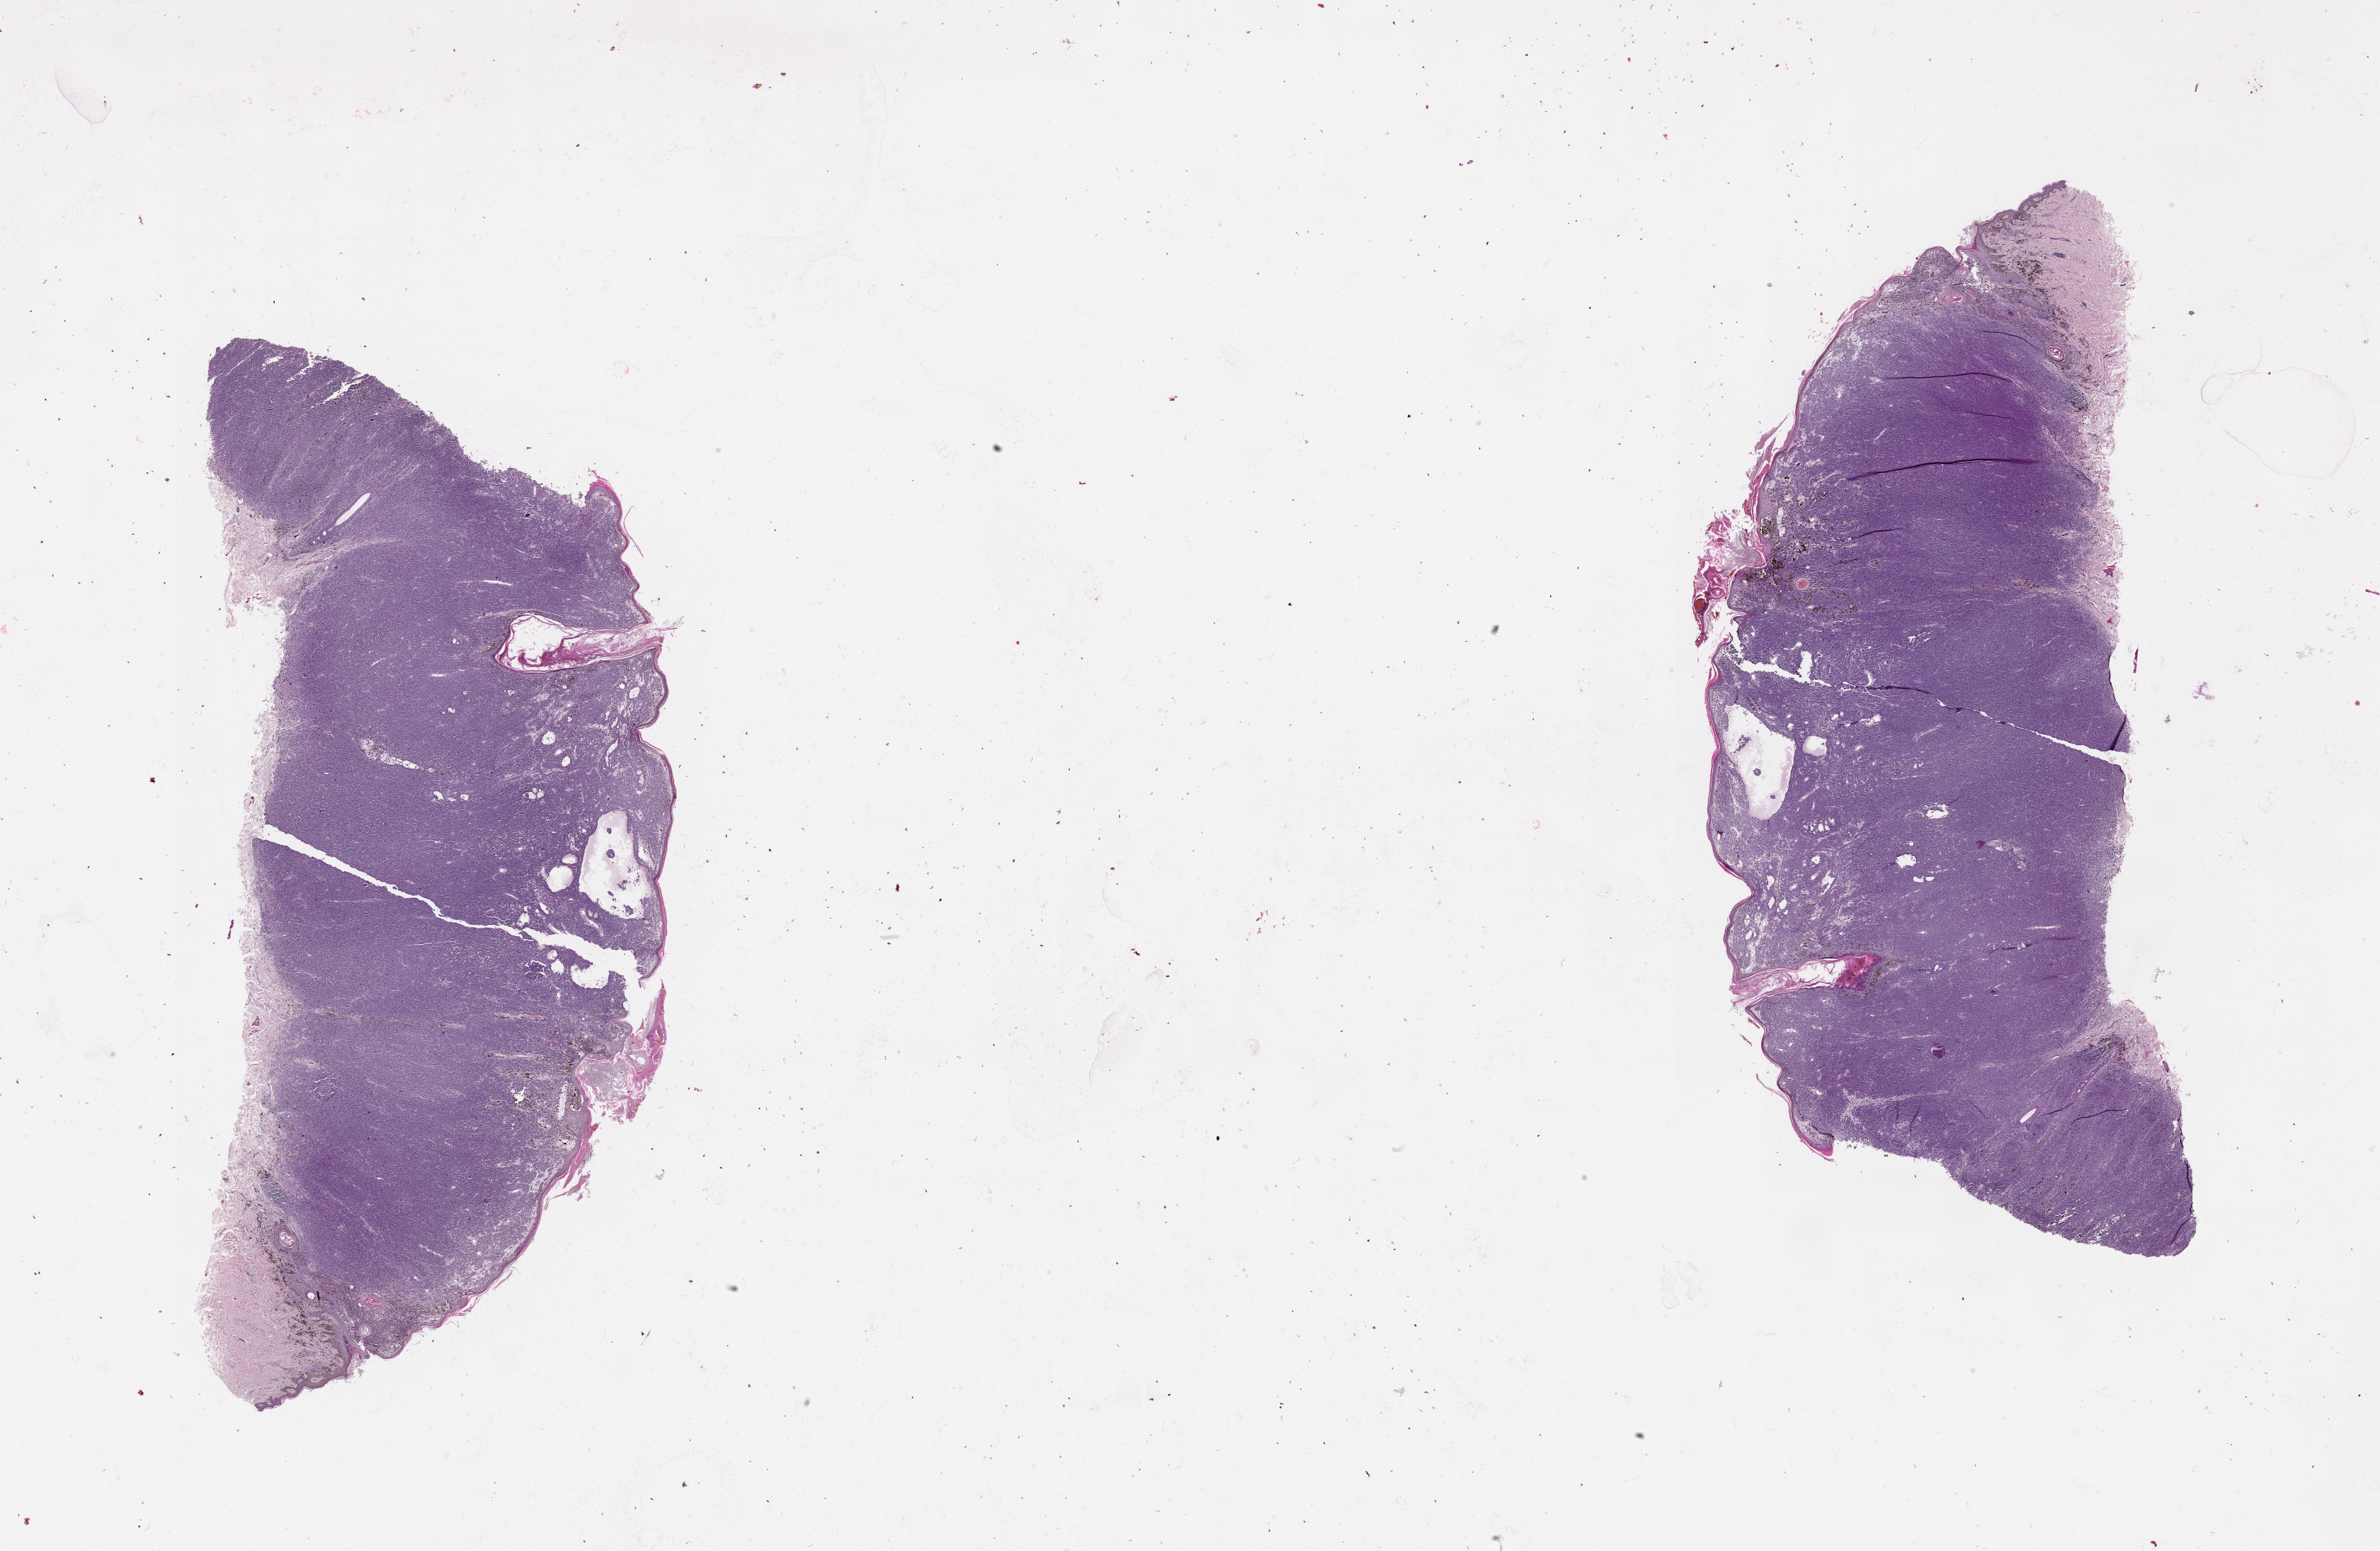
Digitized H&E-stained tissue section (whole slide) — shown as a low-resolution overview of the whole scanned area (about 27.1 x 17.6 mm, acquisition: 20x scan), tumour tissue sample, sampled site: back. Female, 74 y/o. Slide review estimates, as recorded: tumour nuclei 80%, necrosis 0%.
* AJCC pathologic stage: IIC
* histologic diagnosis: Malignant melanoma, NOS